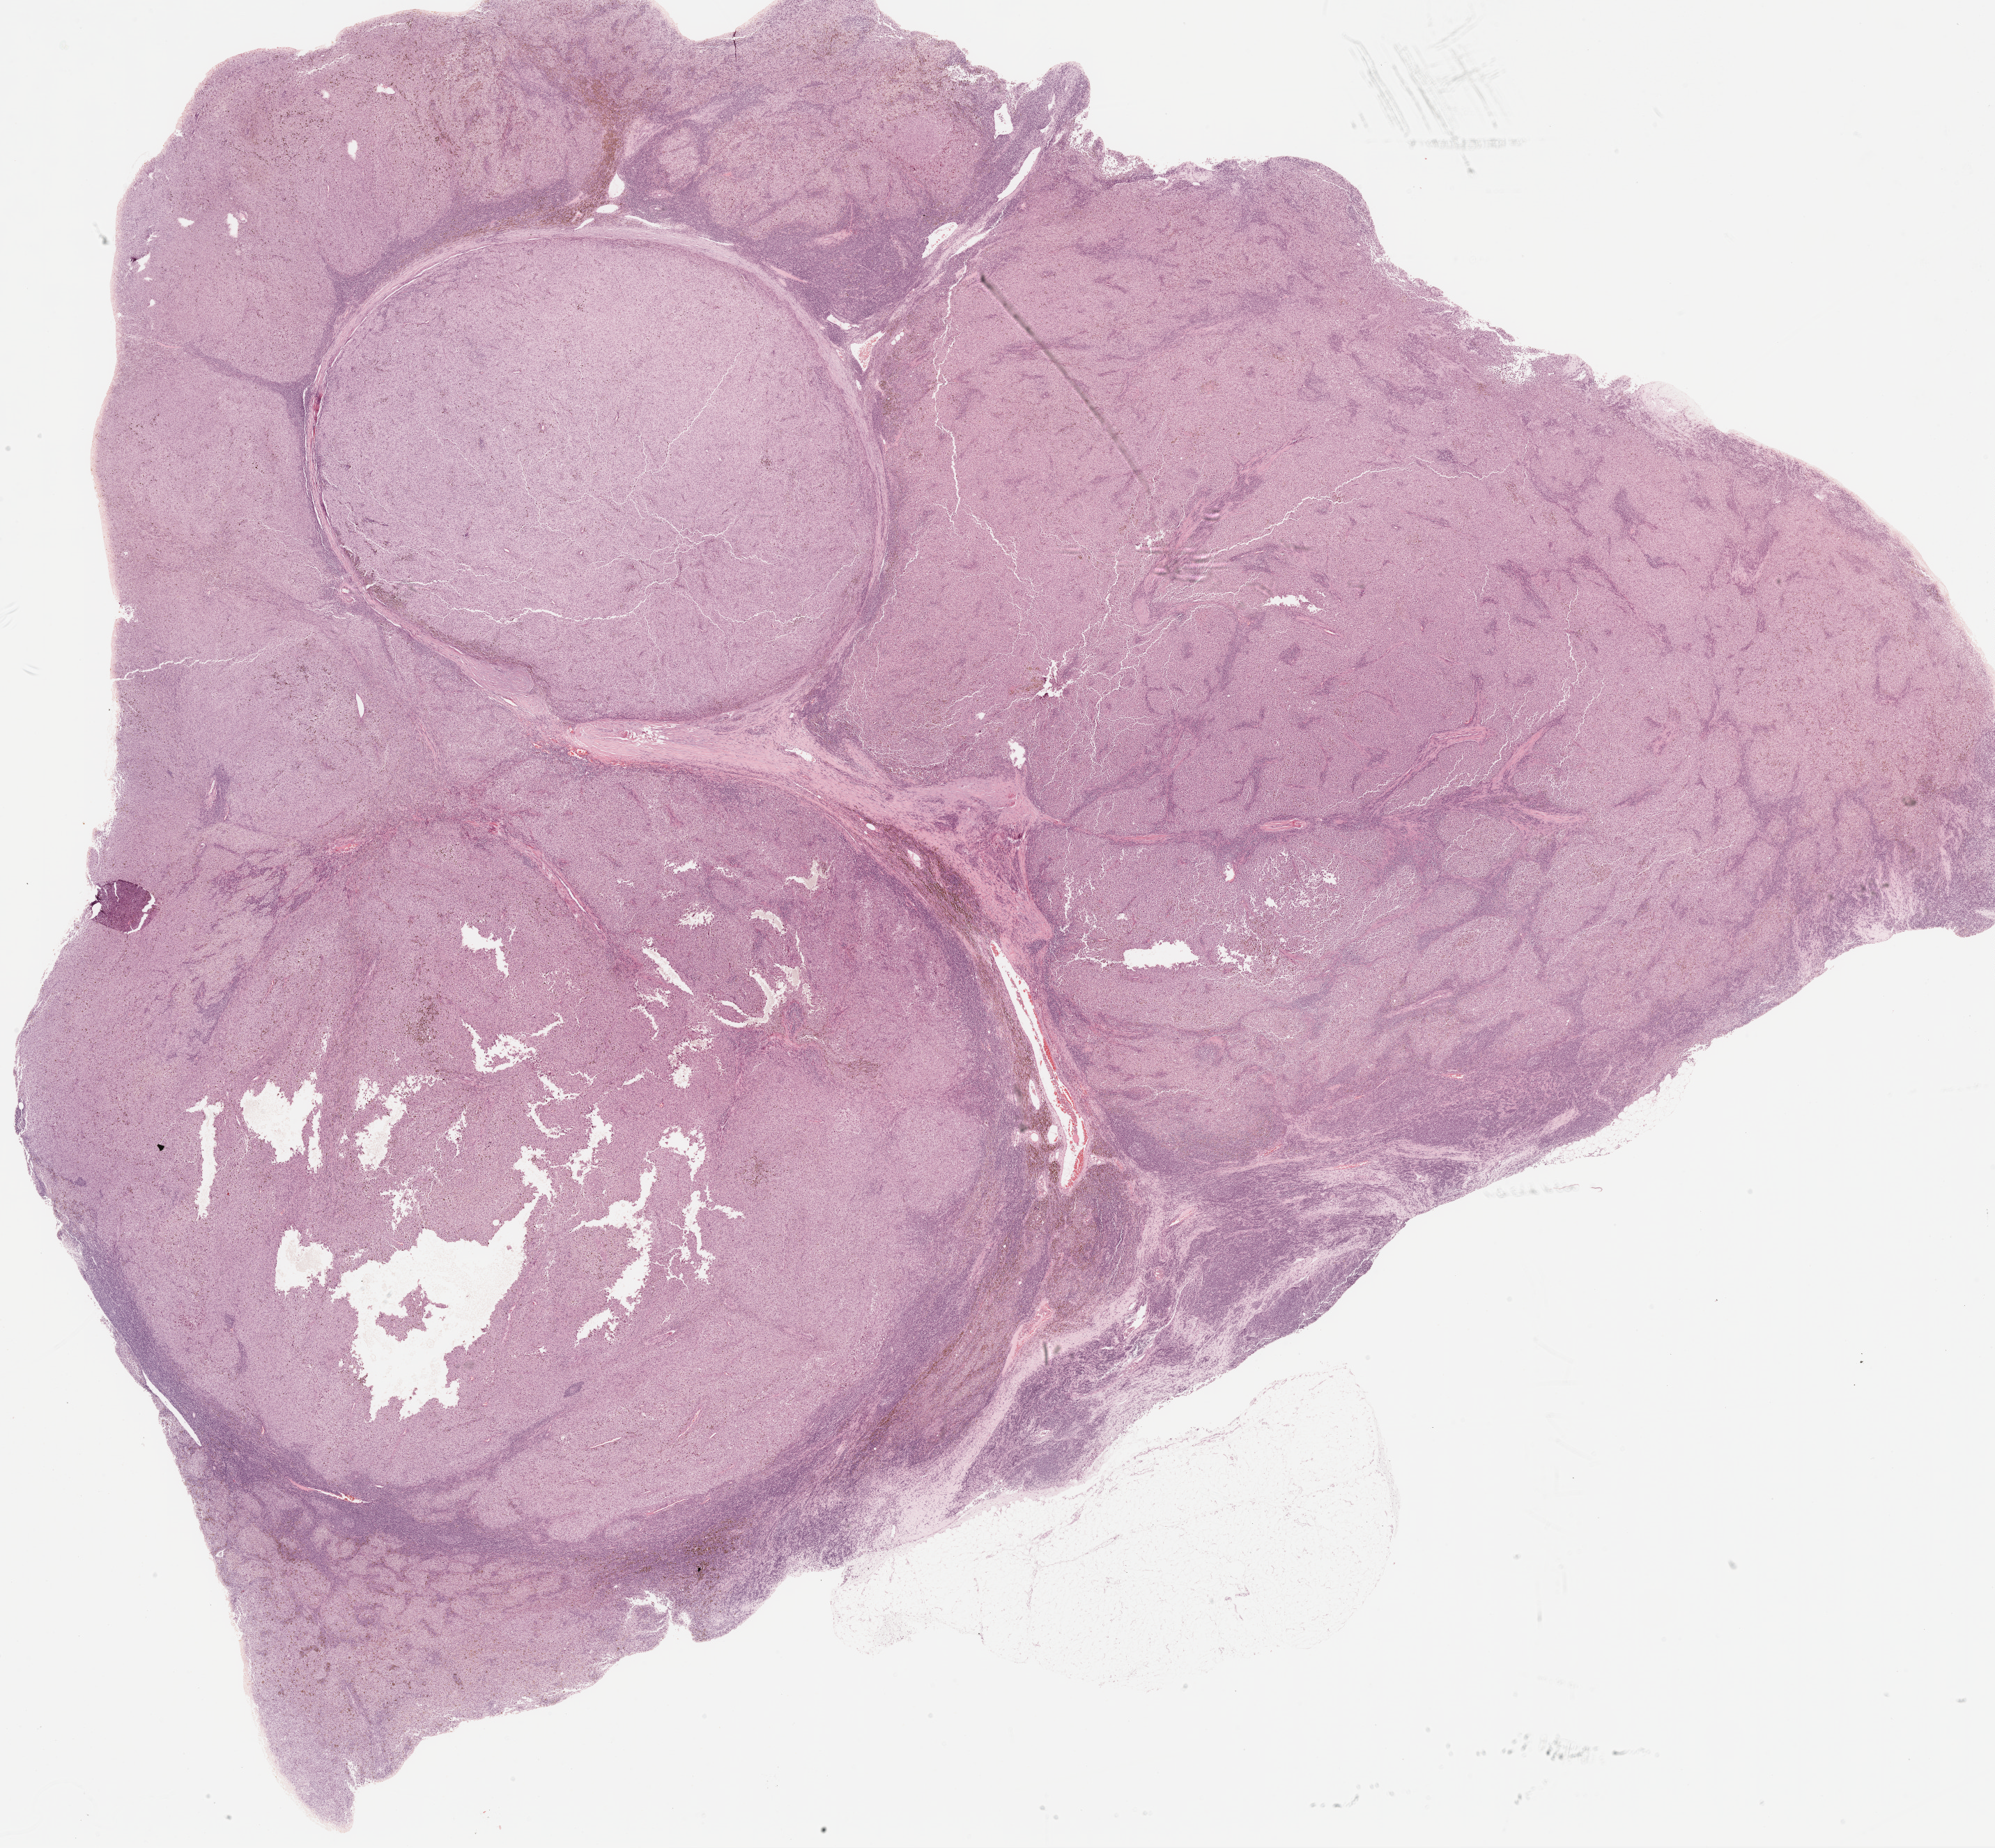
Whole-slide histology image, H&E, low-resolution overview of the scanned area, about 23.1 x 21.4 mm (slide scanned at 20x). Formalin-fixed paraffin-embedded (FFPE) diagnostic section. Metastatic tumour sample, sampled site: lymph nodes of axilla or arm. Male patient; age at initial diagnosis 39 years.
* this section: metastatic tumour tissue
* patient diagnosis: Malignant melanoma, NOS